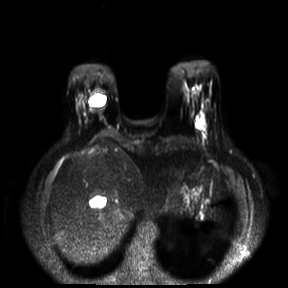
Breast MRI, one axial slice. Slice 4 of 30 in the series (ordered by position). Diffusion-weighted series; image 2 of 4 stored at this slice position (different b-values; order by instance number). 3 T. 288 × 288 image matrix. Female patient.
Structures marked on this image (expert manual segmentation):
- tumour on diffusion-weighted imaging: box from (x=196, y=121) to (x=204, y=128) px